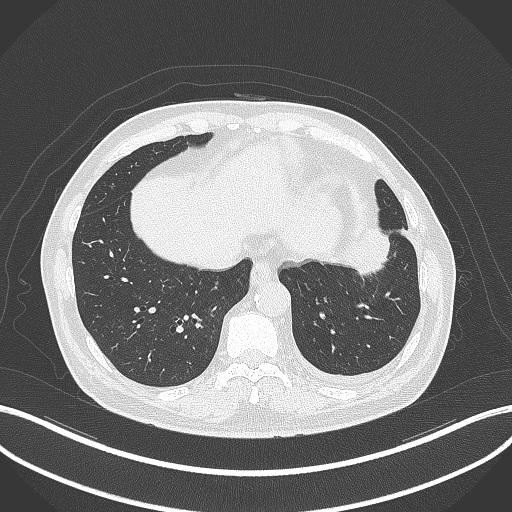
Chest CT, one axial slice; 120 kVp; lung window (W 1500 / L -600 HU); 512 × 512 image matrix, field of view 400 × 400 mm. Male patient, age 68 years. Case-level facts recorded for this patient, not image findings: clinical TNM (as recorded): T2b N0 M0.
Structures marked on this image (bounding box drawn by a radiologist):
- lung tumour (recorded histology: squamous cell carcinoma): bounding box <344,223,395,281> (left, top, right, bottom; pixels)